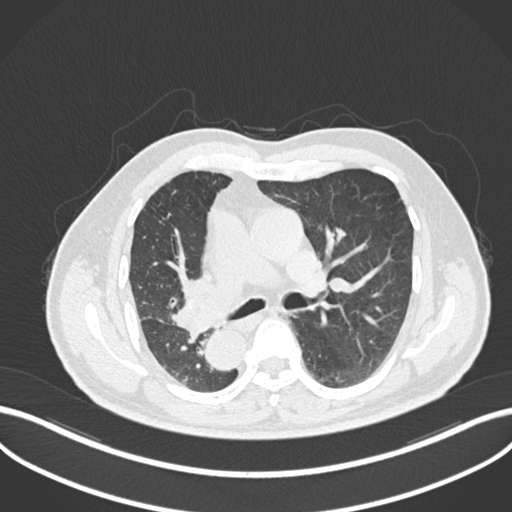
Chest CT, one axial slice. Slice 135 of 206 in the series (ordered by position). 120 kVp. Lung window (W 1500 / L -600 HU). 1 mm slice thickness. 512 × 512 image matrix, field of view 400 × 400 mm. Male patient, age 67 years. From the clinical record (not read from this slice): clinical TNM (as recorded): T2a N0 M0.
Structures marked on this image (rectangle marked by the reading radiologist):
- lung tumour (recorded histology: squamous cell carcinoma): box from (x=165, y=275) to (x=227, y=334) px